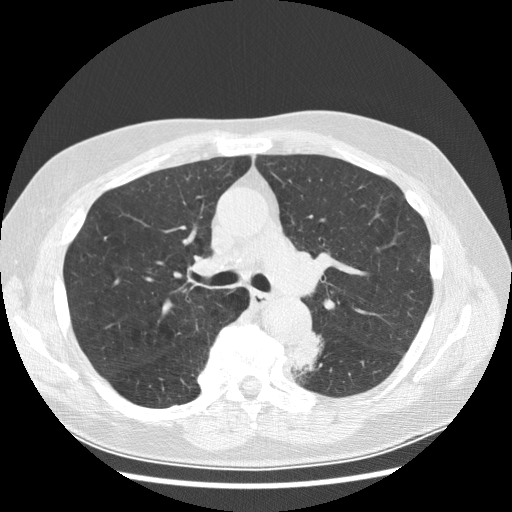
Low-dose screening chest CT, axial slice. Baseline screening round. Lung window (W 1500 / L -600 HU). Standard (soft-tissue) reconstruction kernel (STANDARD). Slice 100 of 282 in the series. Male, age 70 years at enrolment. Current smoker at enrolment.
Lesion marked by an expert reader, bounding box (x1, y1, x2, y2) in pixels: (277, 333, 327, 381). Screening reader's record for this exam (one nodule recorded; not confirmed to be the boxed lesion): non-calcified nodule or mass ≥4 mm, left lower lobe, 27 × 16 mm, spiculated (stellate) margins, soft tissue attenuation, pre-existing on the prior screen: yes; interval growth: yes. Official screen result: positive, change unspecified: nodule(s) >= 4 mm or enlarging nodule(s), mass(es), or other non-specific abnormalities suspicious for lung cancer.